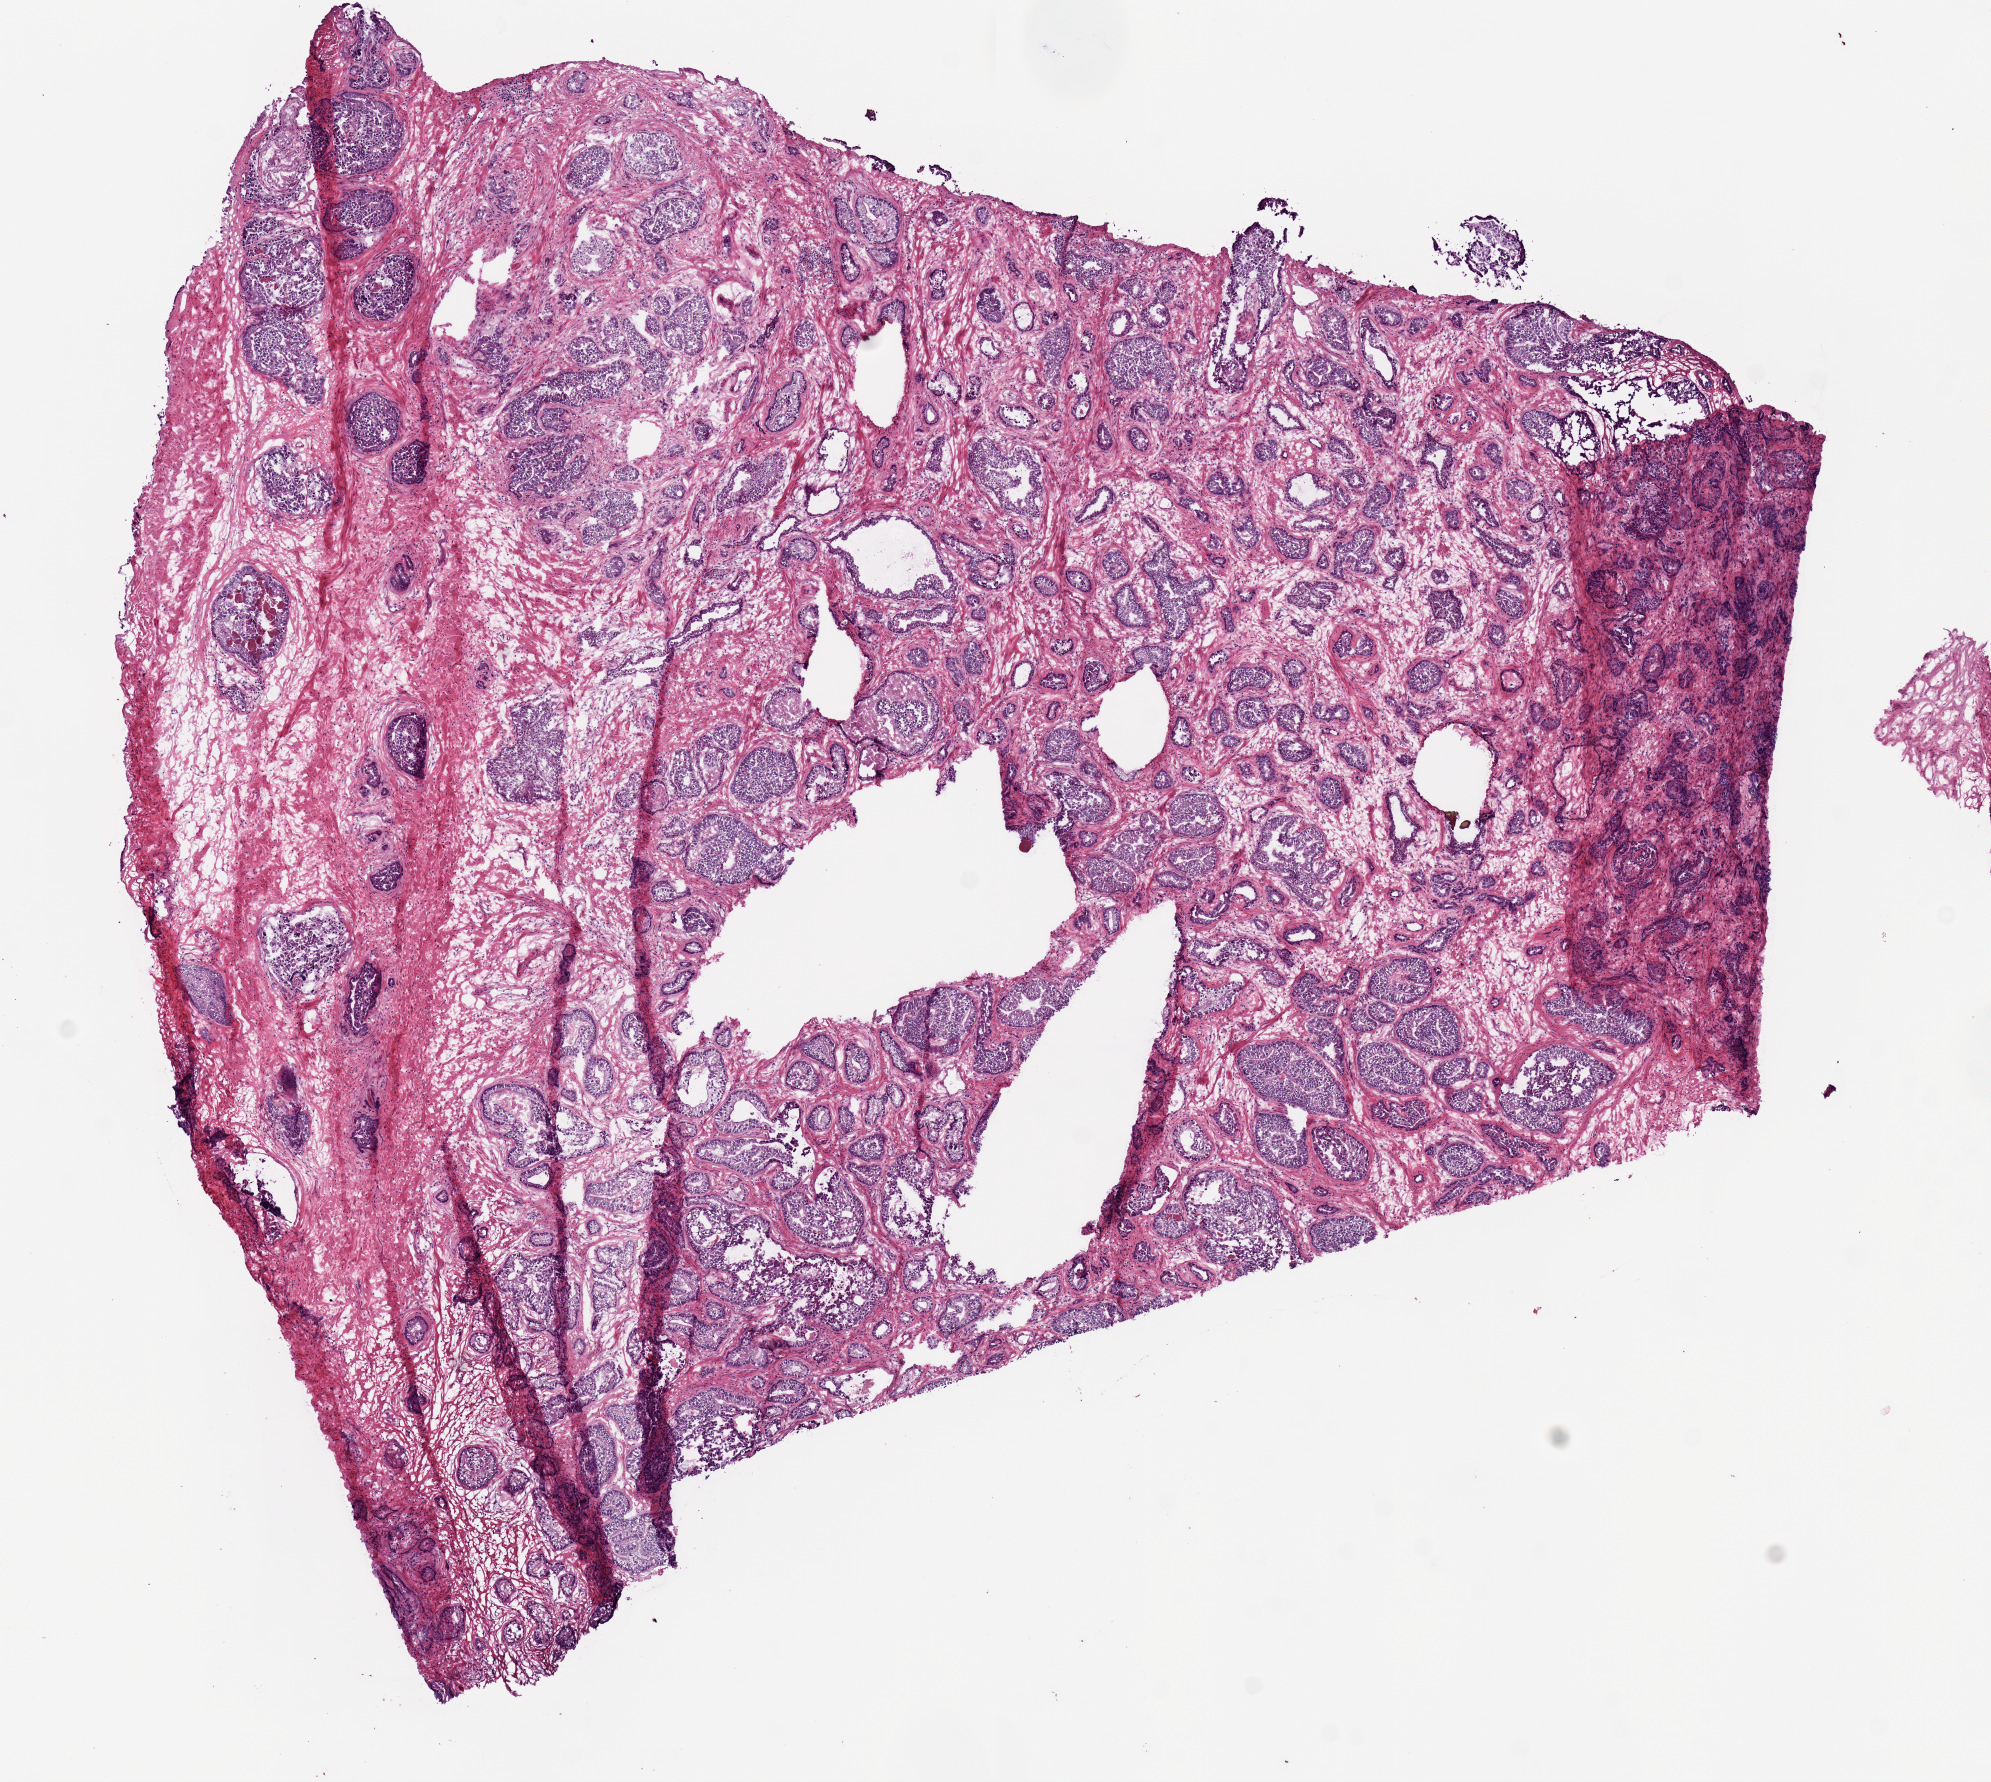
Whole-slide histology image, Hematoxylin and eosin (H&E) stained, shown as a low-resolution overview of the whole scanned area (about 7.9 x 7.0 mm, from a 20x scan), frozen section, sample: primary tumour, prostate. Male, age 62 years at initial diagnosis. Gleason score: 7 (4+3). Pathologist review of this section (percent, as recorded): tumour cells 65%, tumour nuclei 65%, normal cells 10%, stromal cells 25%, necrosis 0%.
* pathologic diagnosis: Acinar cell carcinoma
* lymph nodes positive (case pathology): 0 of 14 examined